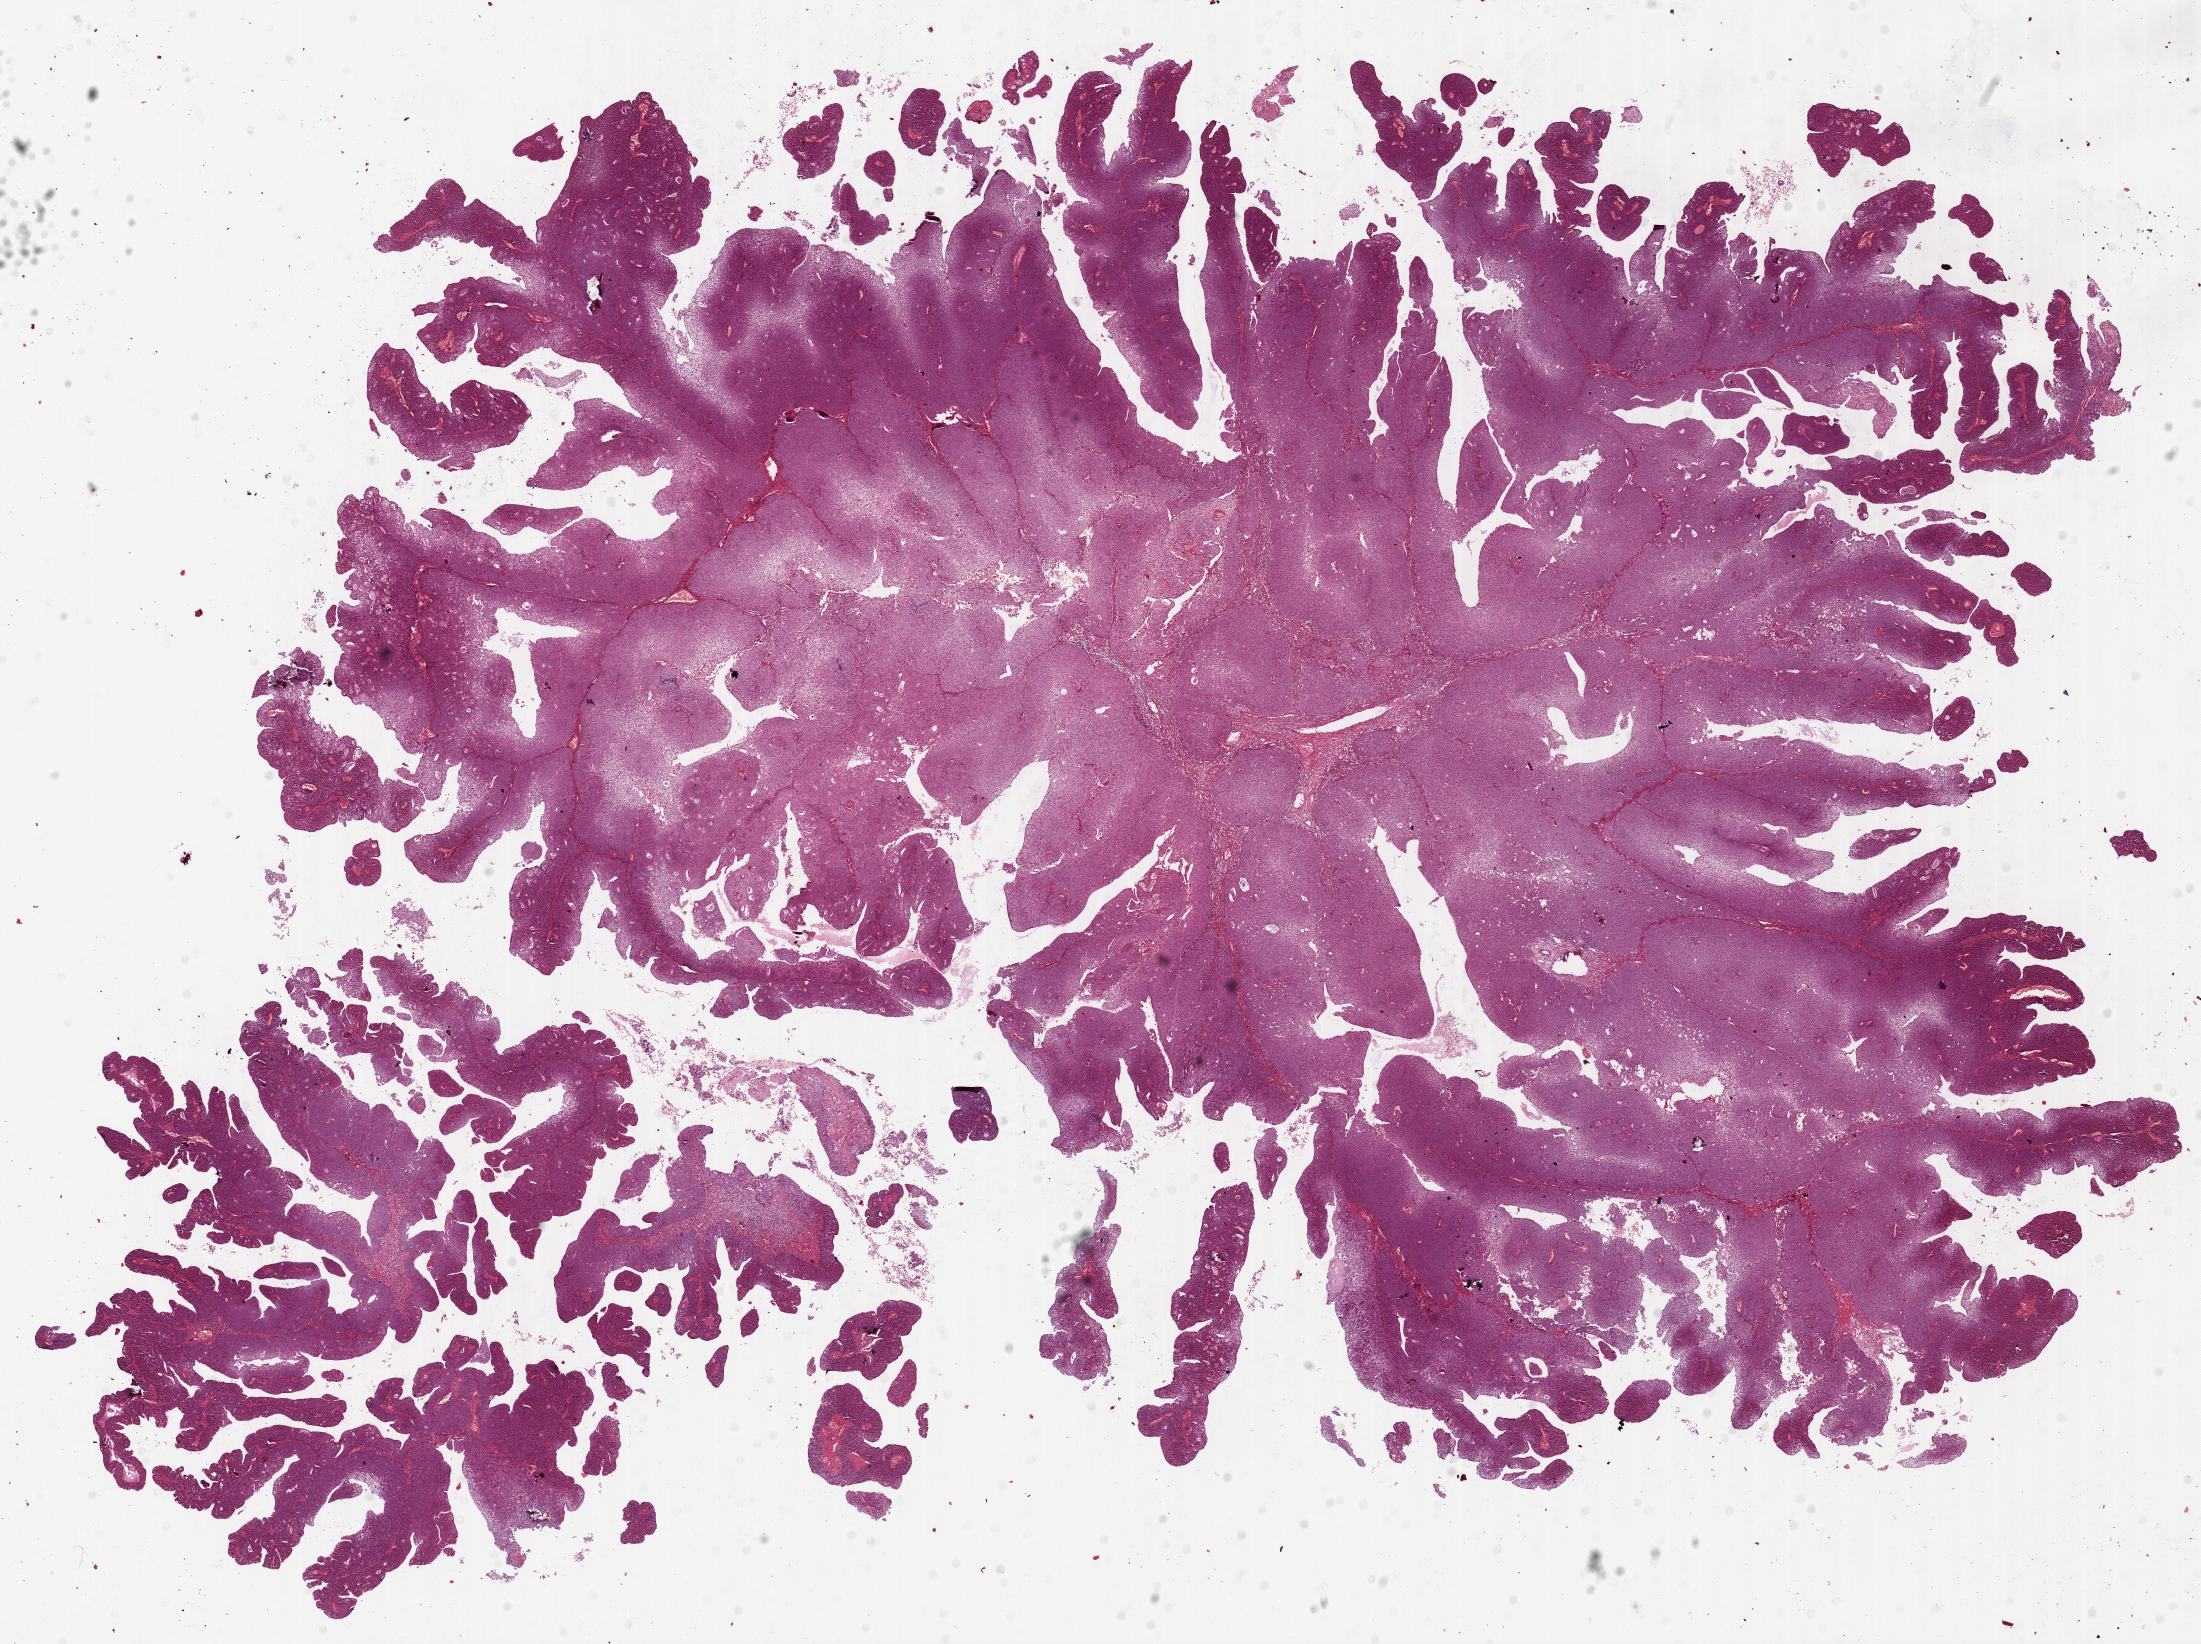
Whole-slide histology image, H&E-stained, a low-resolution overview of the entire scanned area, about 17.4 x 13.0 mm (from a 40x scan). Formalin-fixed paraffin-embedded (FFPE) diagnostic section. Bladder, primary tumour sample. Male patient; age at initial diagnosis 52 years. Histologic grade: high grade.
- AJCC pathologic stage: III (6th edition)
- diagnosis: Papillary transitional cell carcinoma